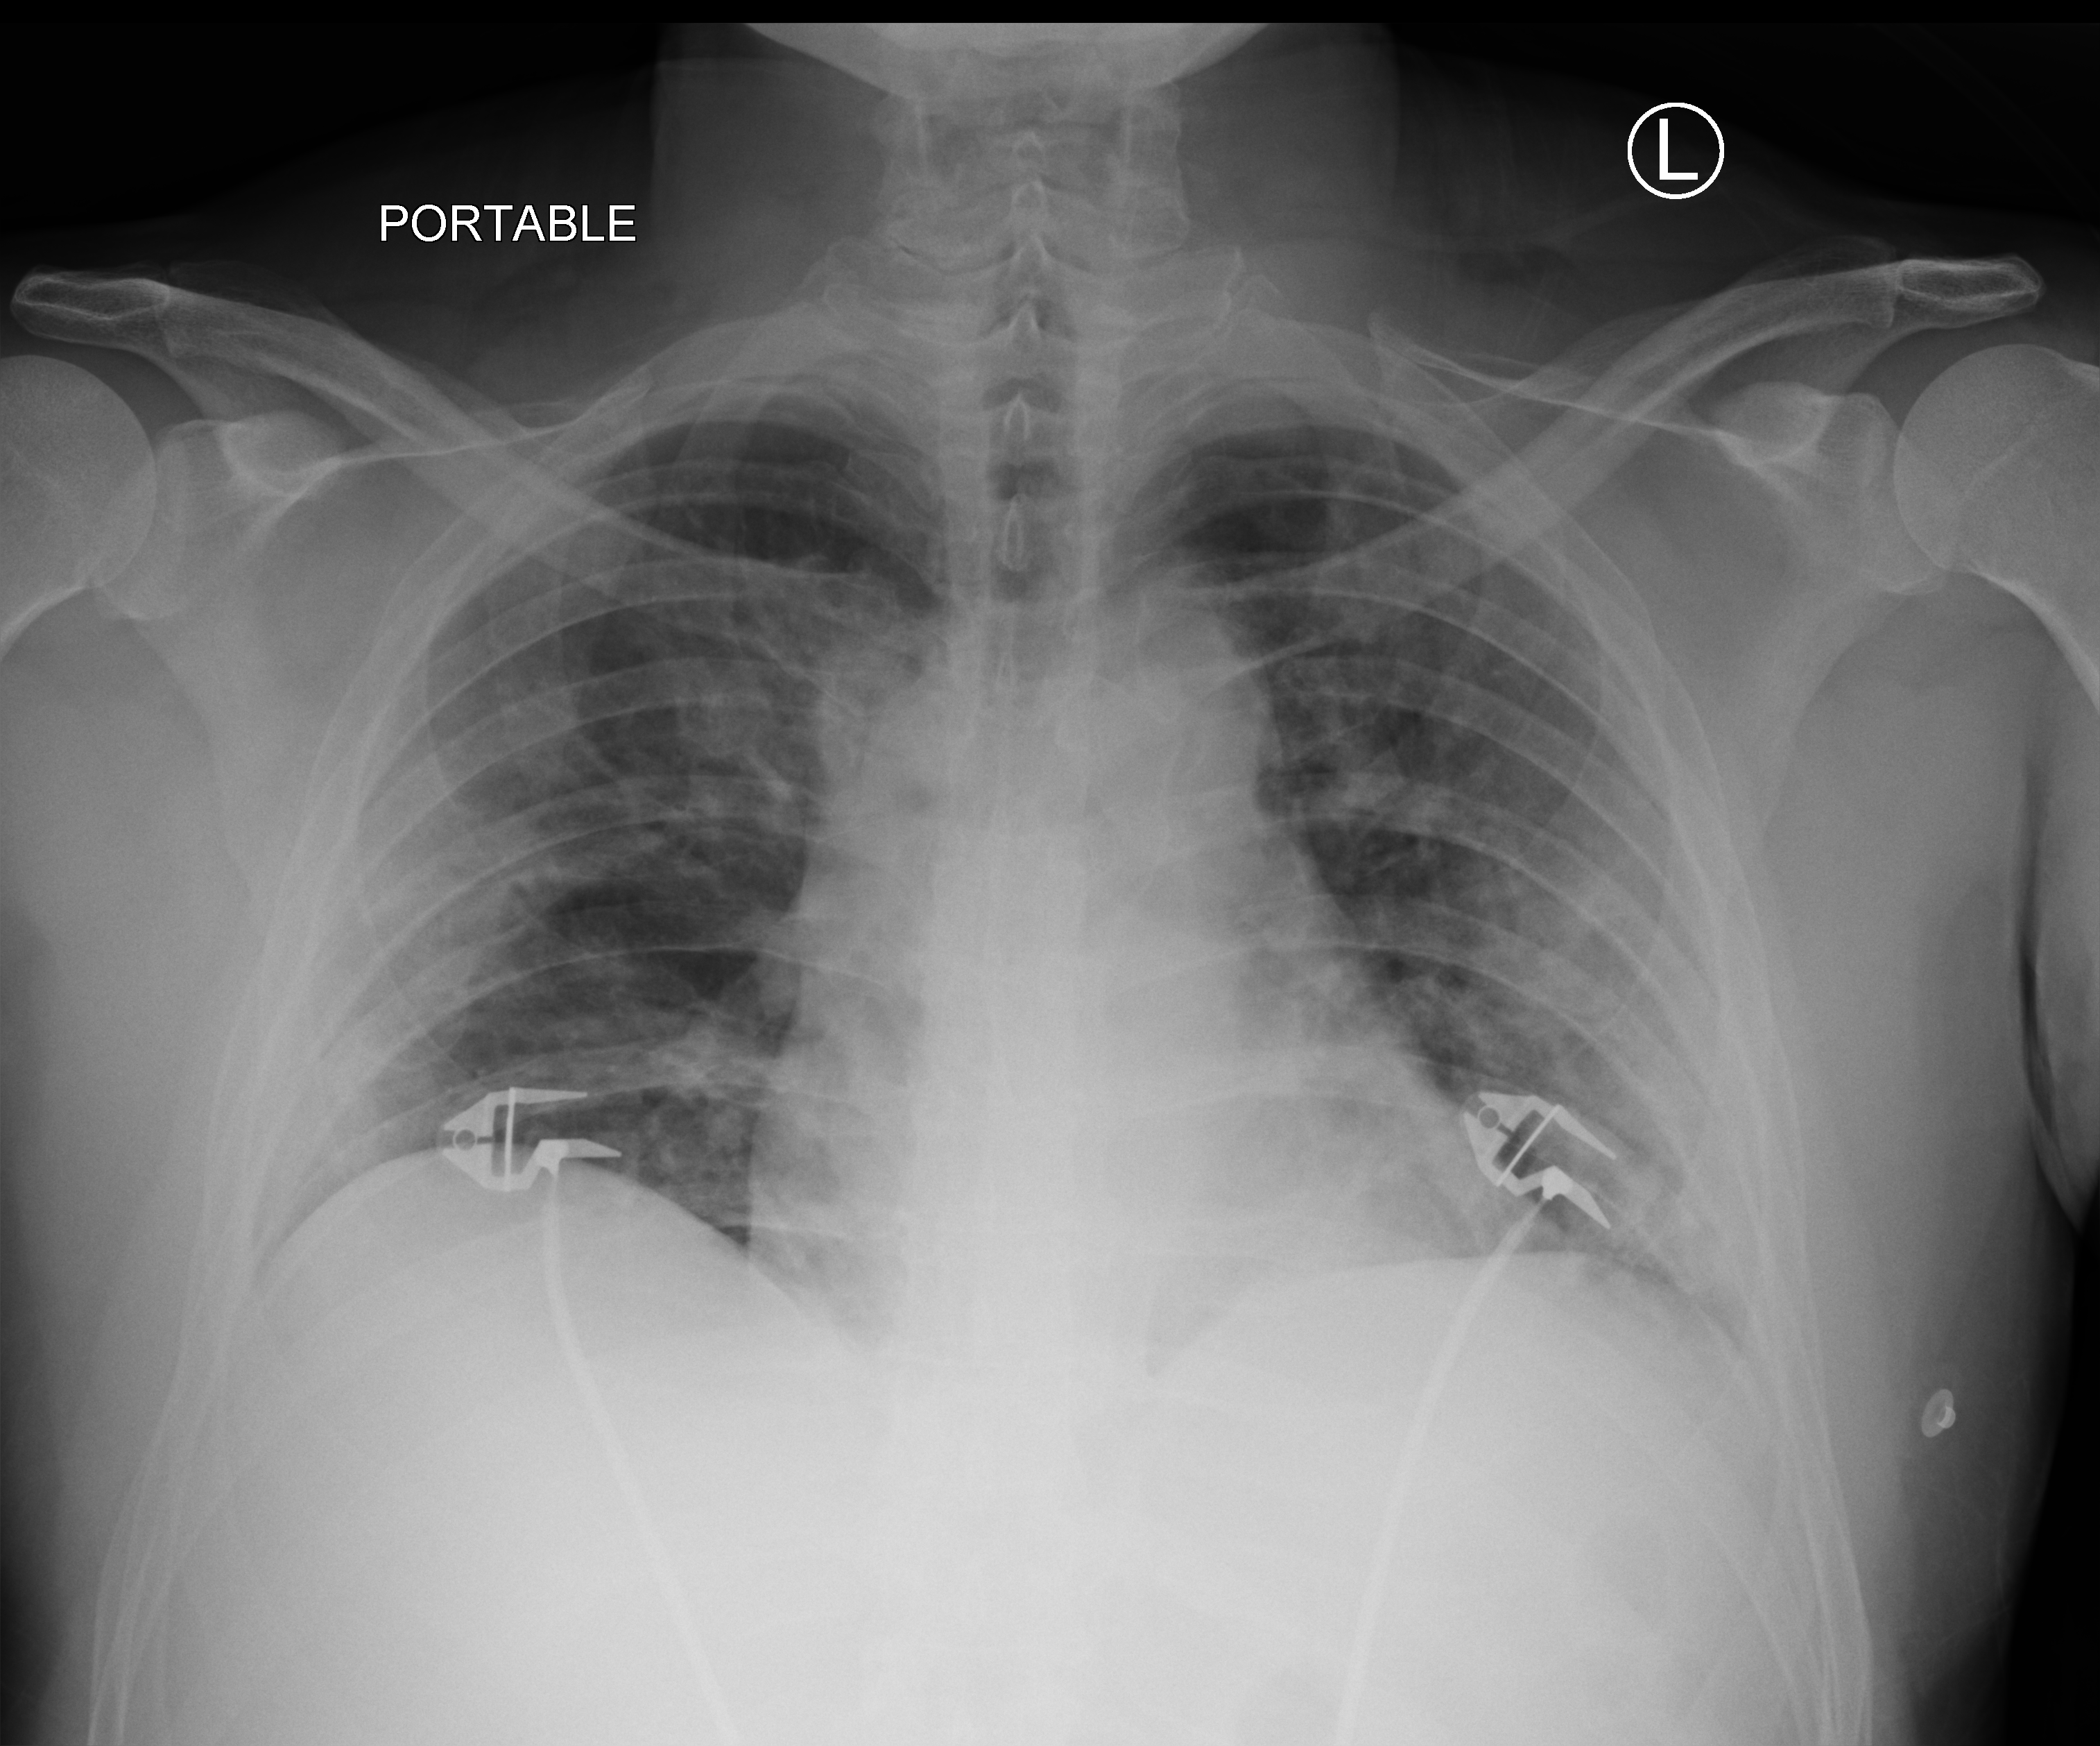
Bedside chest radiograph (computed radiography), anteroposterior (AP) projection. Patient hospitalised with COVID-19; male, aged 18–59 years.
Hospital-stay facts (about this admission, not read from this image; timing relative to this image not recorded):
- admitted to intensive care during this hospital stay: yes
- length of hospital stay: 24 days